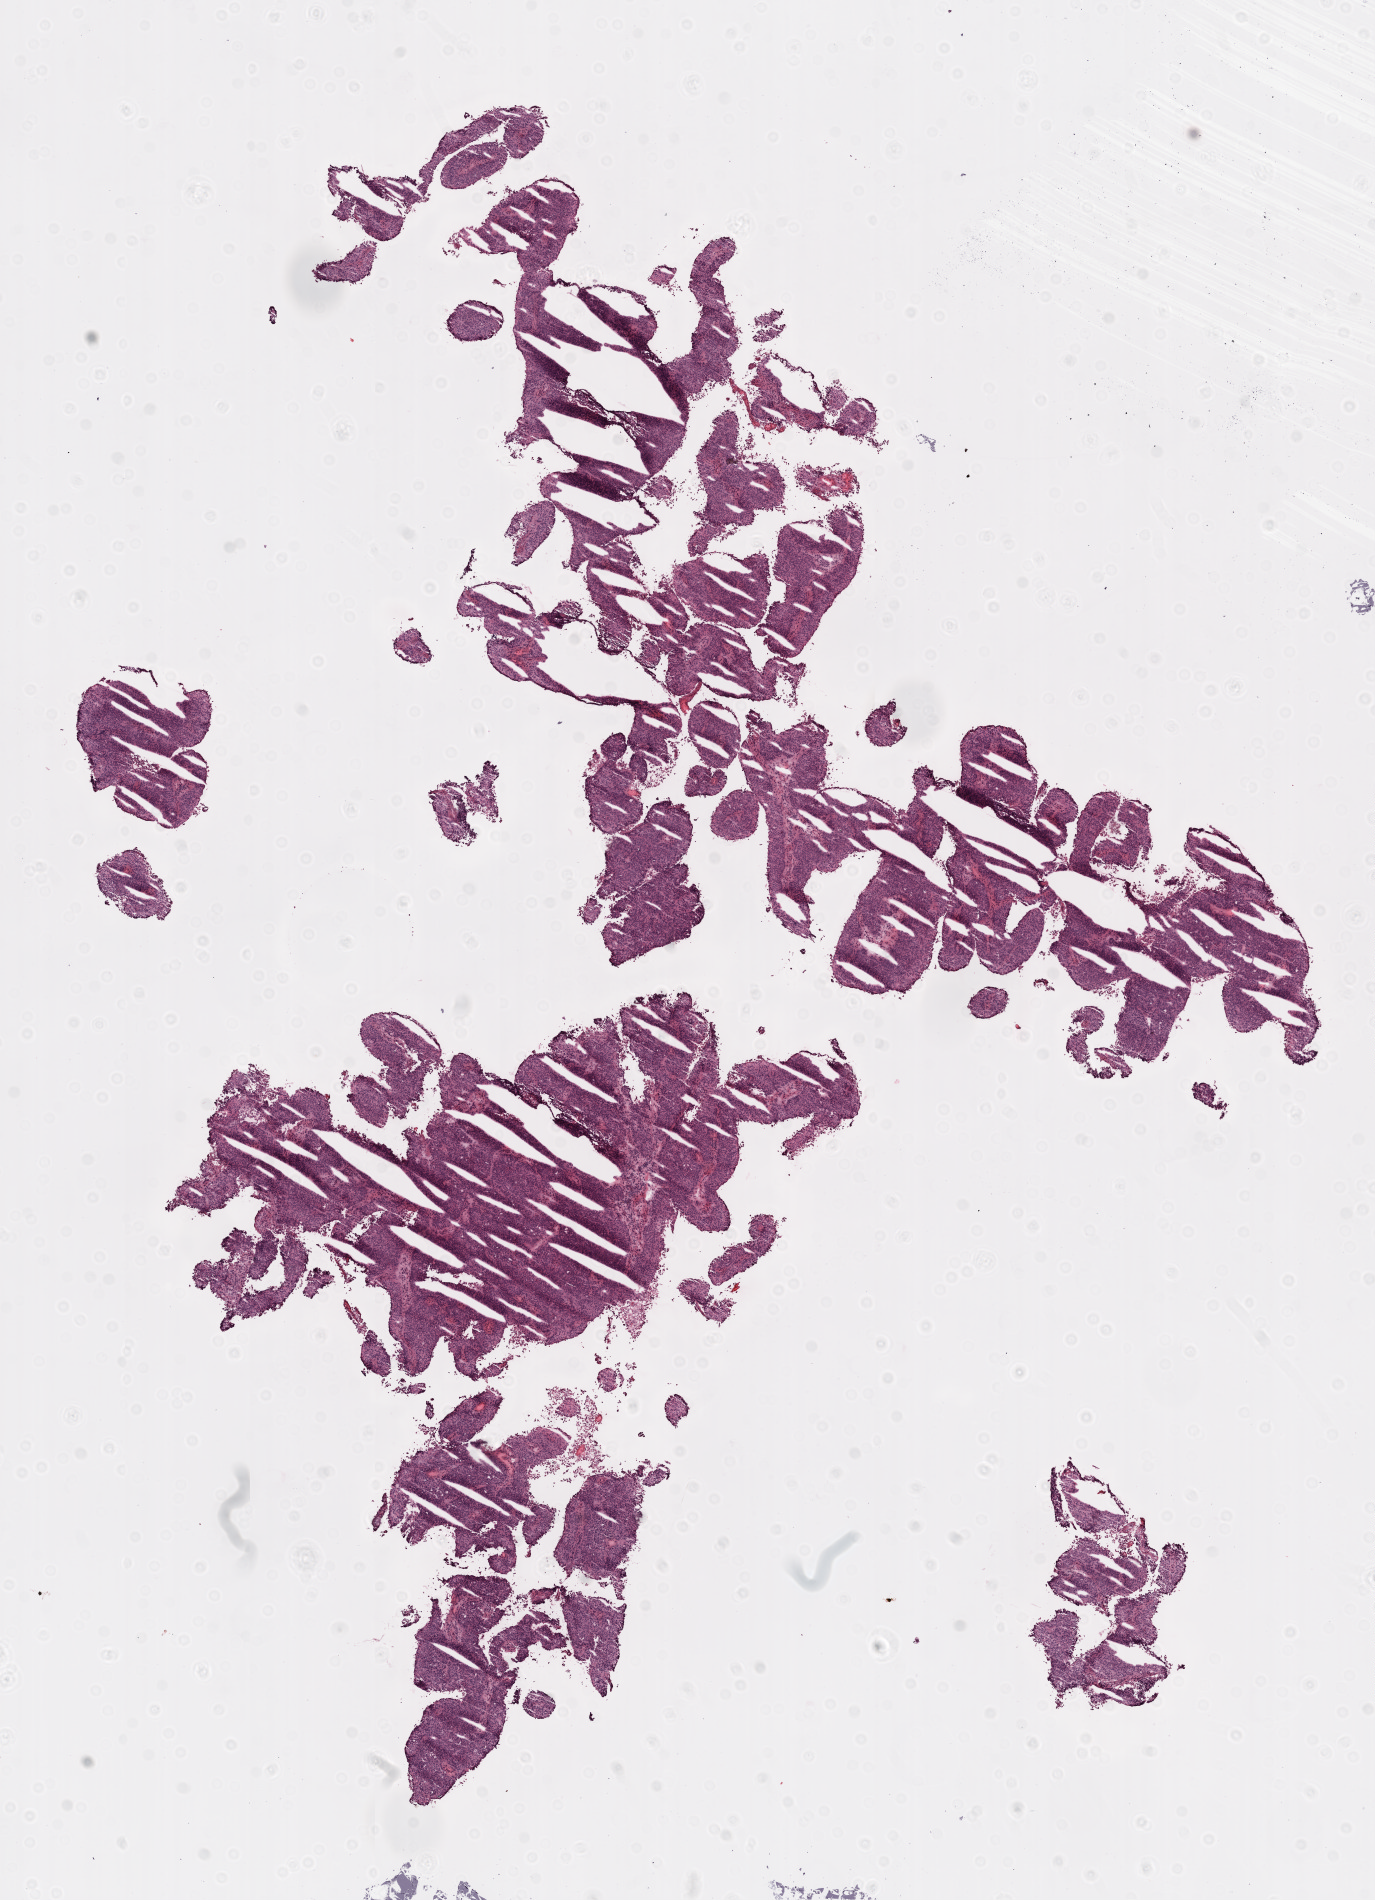
Digitized H&E-stained tissue section (whole slide), whole scanned area (about 11.0 x 15.2 mm, slide scanned at 20x) shown as a low-resolution overview. Frozen section. Ovary, recurrent tumour sample. Female, age 41 years at initial diagnosis. Slide review estimates, as recorded: tumour cells 90%, tumour nuclei 95%, normal cells 0%, stromal cells 10%, necrosis 0%.
This section: recurrent tumour. Patient diagnosis: Serous cystadenocarcinoma, NOS.